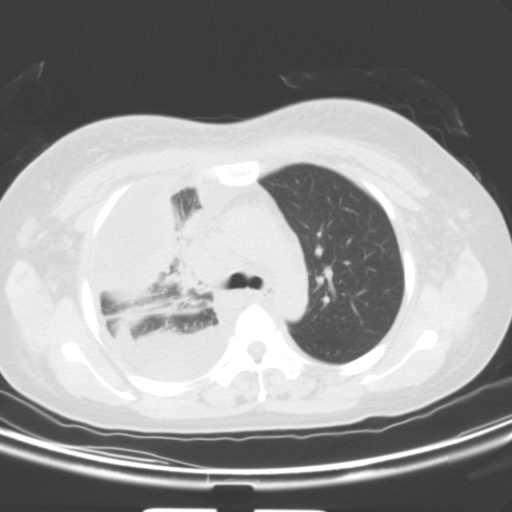
Chest CT, one axial slice. Position 36 of 54 along the scan axis. 120 kVp. Lung window (W 1500 / L -600 HU). 5 mm slice thickness. 512 × 512 image matrix. Female patient, age 36 years. From the clinical record (not read from this slice): clinical TNM (as recorded): T1b N2 M0; histopathological grade: G3.
Outlined on this slice (bounding box drawn by a radiologist):
- lung tumour (recorded histology: adenocarcinoma): bounding box <175,223,222,300> (left, top, right, bottom; pixels)